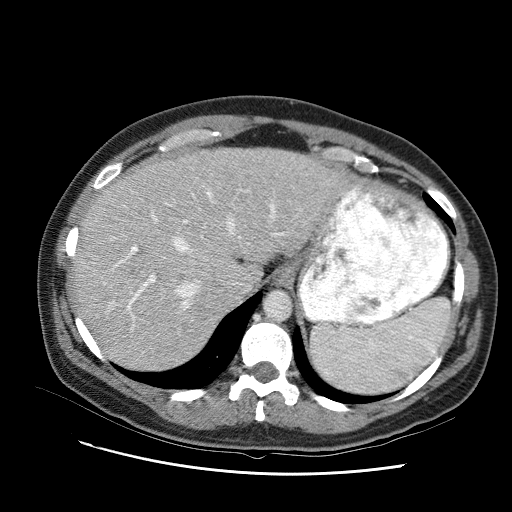
Contrast-enhanced abdominal CT (liver protocol), one axial slice; slice 72 of 95 in the series (ordered by position); one of 2 acquisitions stored at this slice position; soft-tissue window (W 400 / L 40 HU); 2.5 mm slice thickness; 512 × 512 image matrix, field of view 360 × 360 mm. Case-level facts recorded for this patient, not image findings: diagnosis: hepatocellular carcinoma (patient treated with transarterial chemoembolisation; whether this scan precedes or follows treatment is not stated here); TNM stage (as recorded): Stage-I; Child-Pugh class: B.
Structures marked on this image (semi-automatic segmentation, software-assisted and operator-edited):
- liver parenchyma outside the tumour (the mass and vessels are separate outlines, so this box may not span the whole liver): bounding box (x1, y1, x2, y2) in pixels: (72, 146, 346, 354)
- liver vessels: (96, 176, 327, 300)